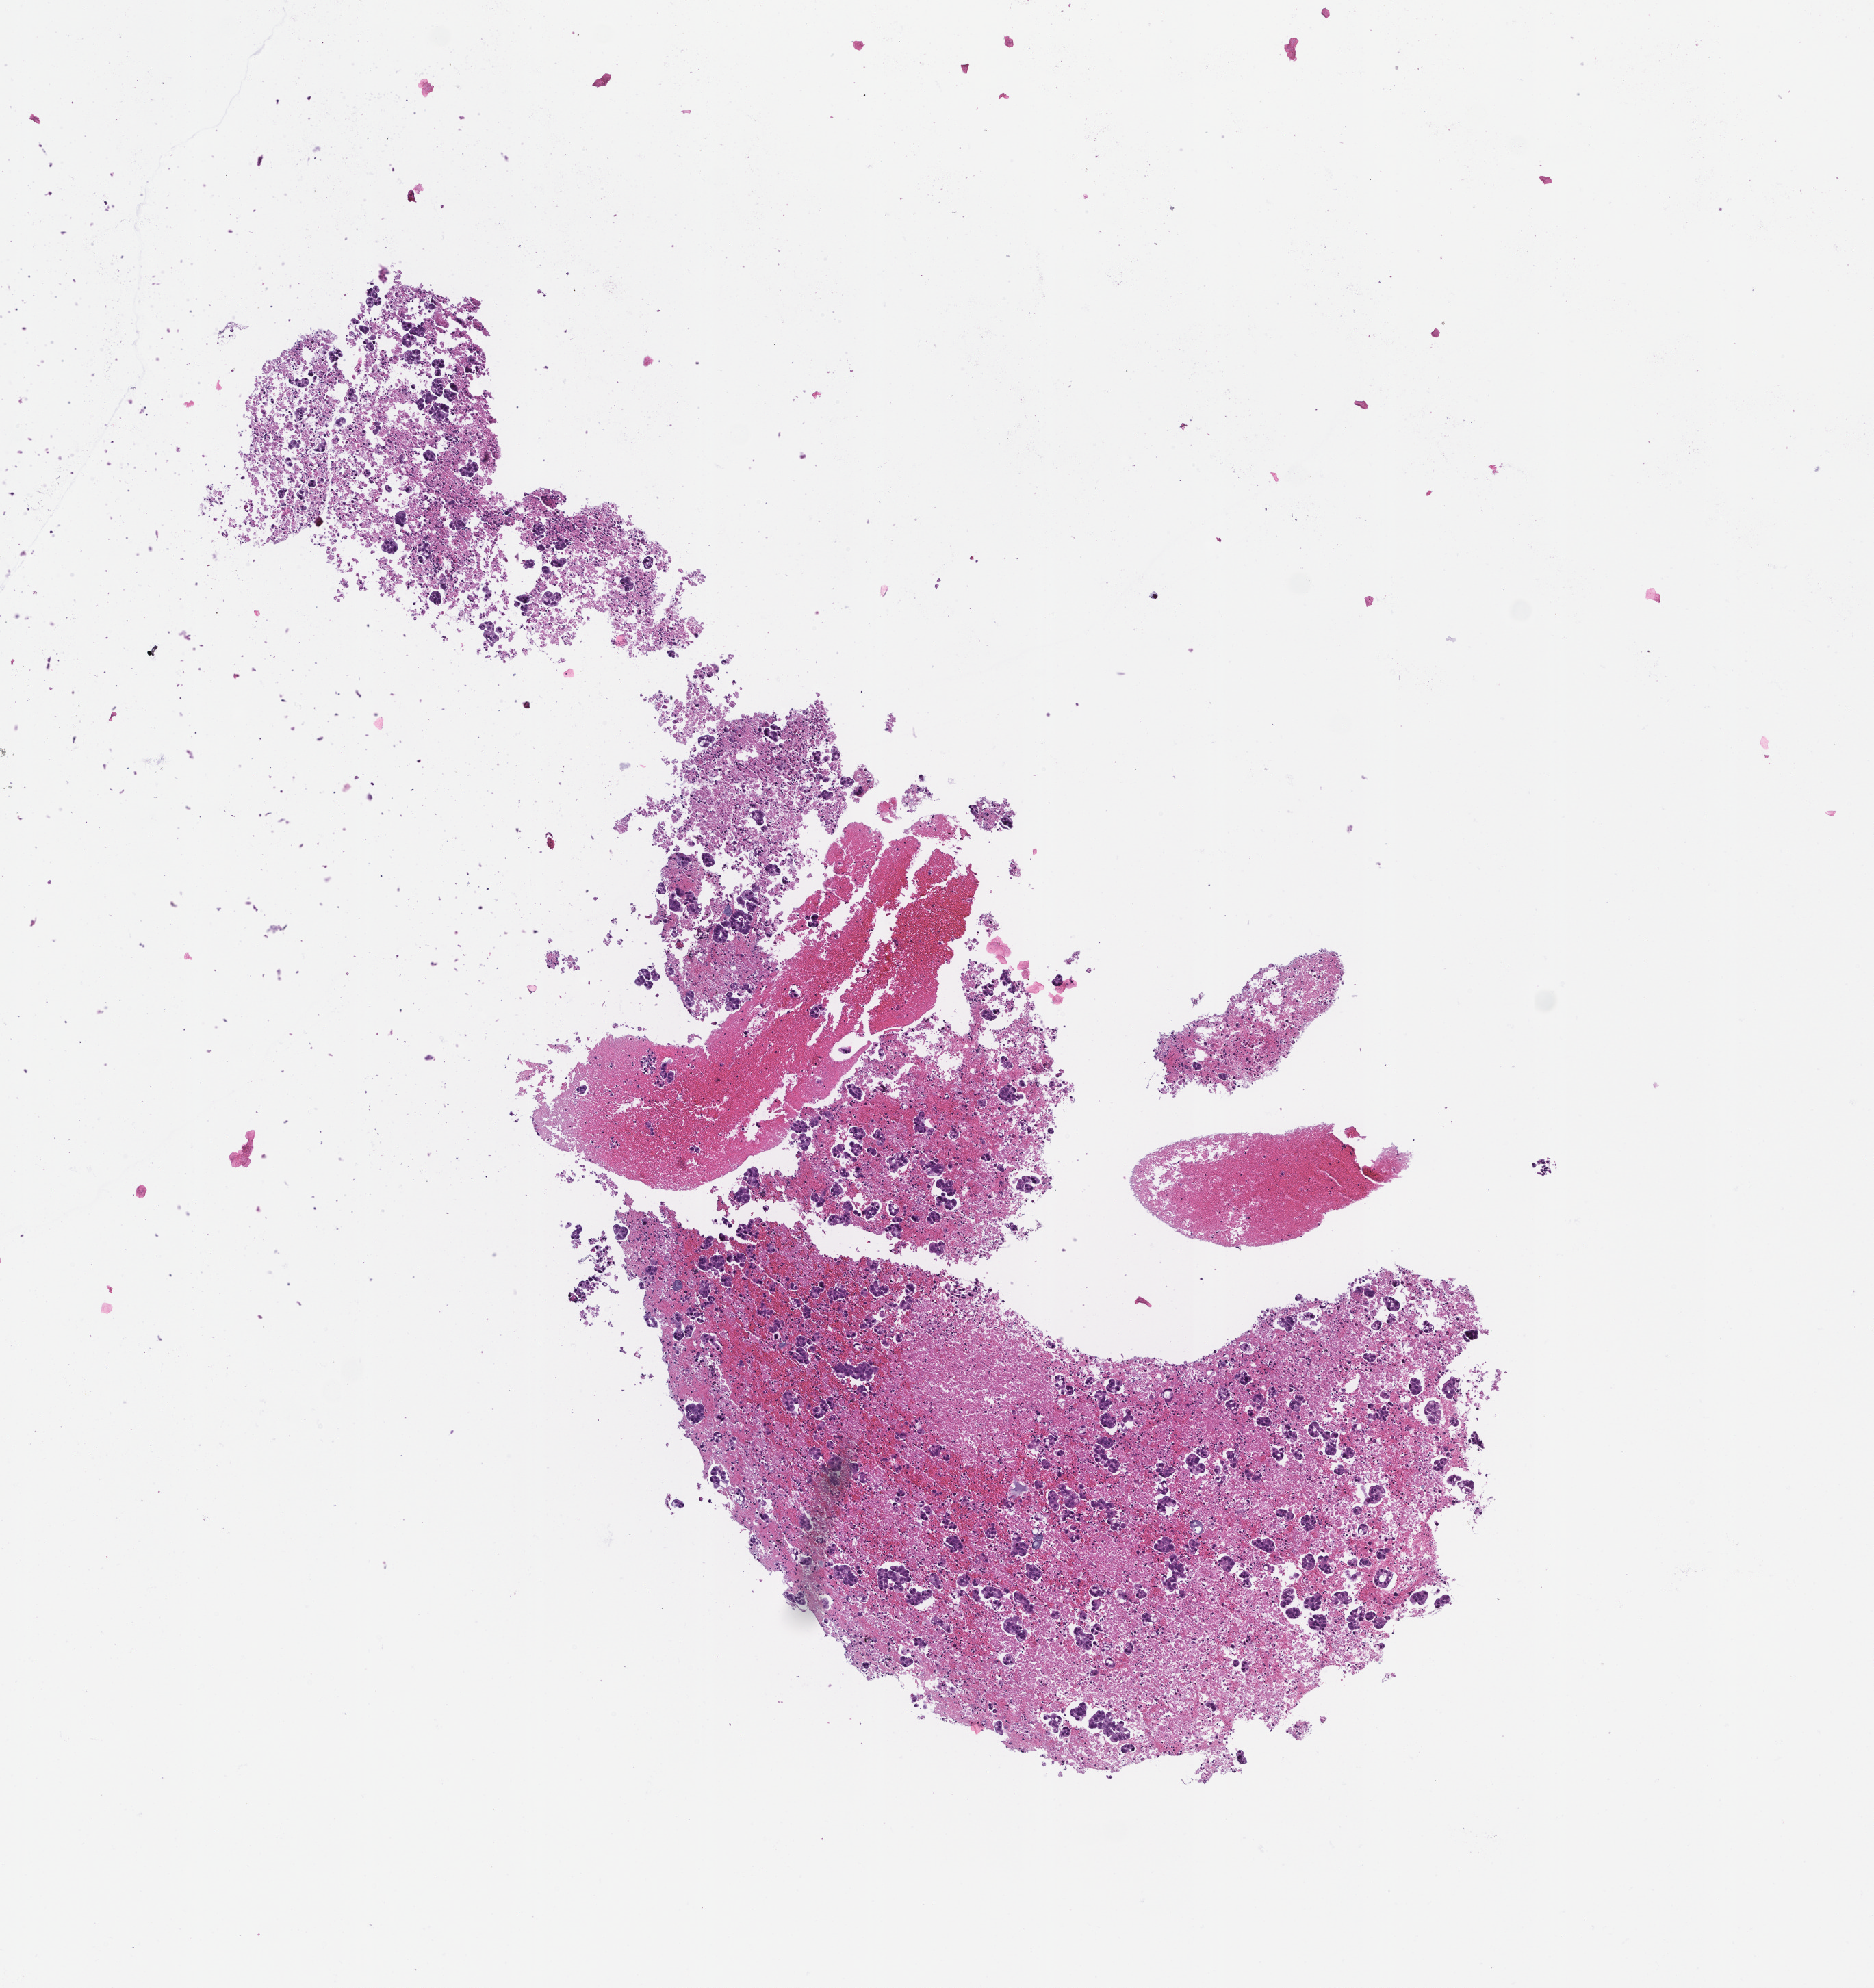
Hematoxylin and eosin (H&E) whole-slide image, low-resolution overview of the scanned area, about 5.5 x 5.9 mm, formalin-fixed, paraffin-embedded (FFPE) tissue, site: lung, archival tissue. Patient sex: male.
This section: primary tumour tissue. Diagnosis: Non-Small Cell Lung Carcinoma.